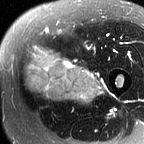
MRI of an extremity soft-tissue mass, one axial slice; position 22 of 60 along the scan axis; T2-weighted fat-saturated; MR volume resampled by the dataset authors to the PET/CT grid (not the native acquisition matrix); 3.27 mm slice thickness; 144 × 144 image matrix, field of view 141 × 141 mm. Female patient. From the clinical record (not read from this slice): histological type: pleiomorphic leiomyosarcoma; grade: intermediate; site of the primary tumour: left thigh.
Structures marked on this image (expert contour drawn on MRI and transferred to this co-registered scan by the dataset authors):
- gross tumour volume including surrounding oedema: box from (x=22, y=47) to (x=108, y=103) px
- gross tumour volume (mass): (x=24, y=47)–(x=99, y=102)